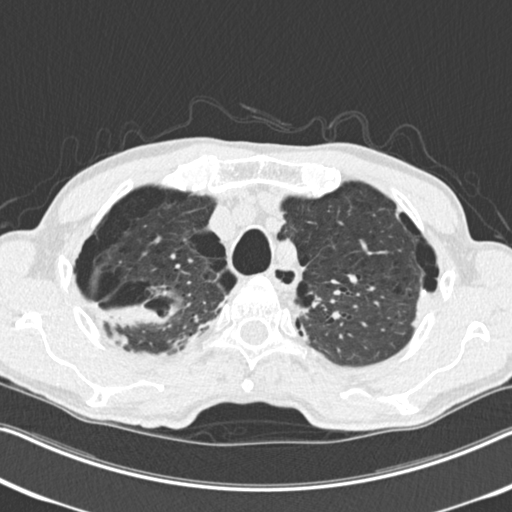
Low-dose screening chest CT, one axial slice. Slice 203 of 251 in the series (ordered by position). Reconstruction kernel B30f. Lung window (W 1500 / L -600 HU). 2 mm slice thickness. 512 × 512 image matrix, field of view 334 × 334 mm.
Annotated regions visible in this slice (expert manual segmentation):
- lesion 1 (tumor, upper lobe of right lung): bounding box [x1, y1, x2, y2] px = [100, 305, 164, 326]